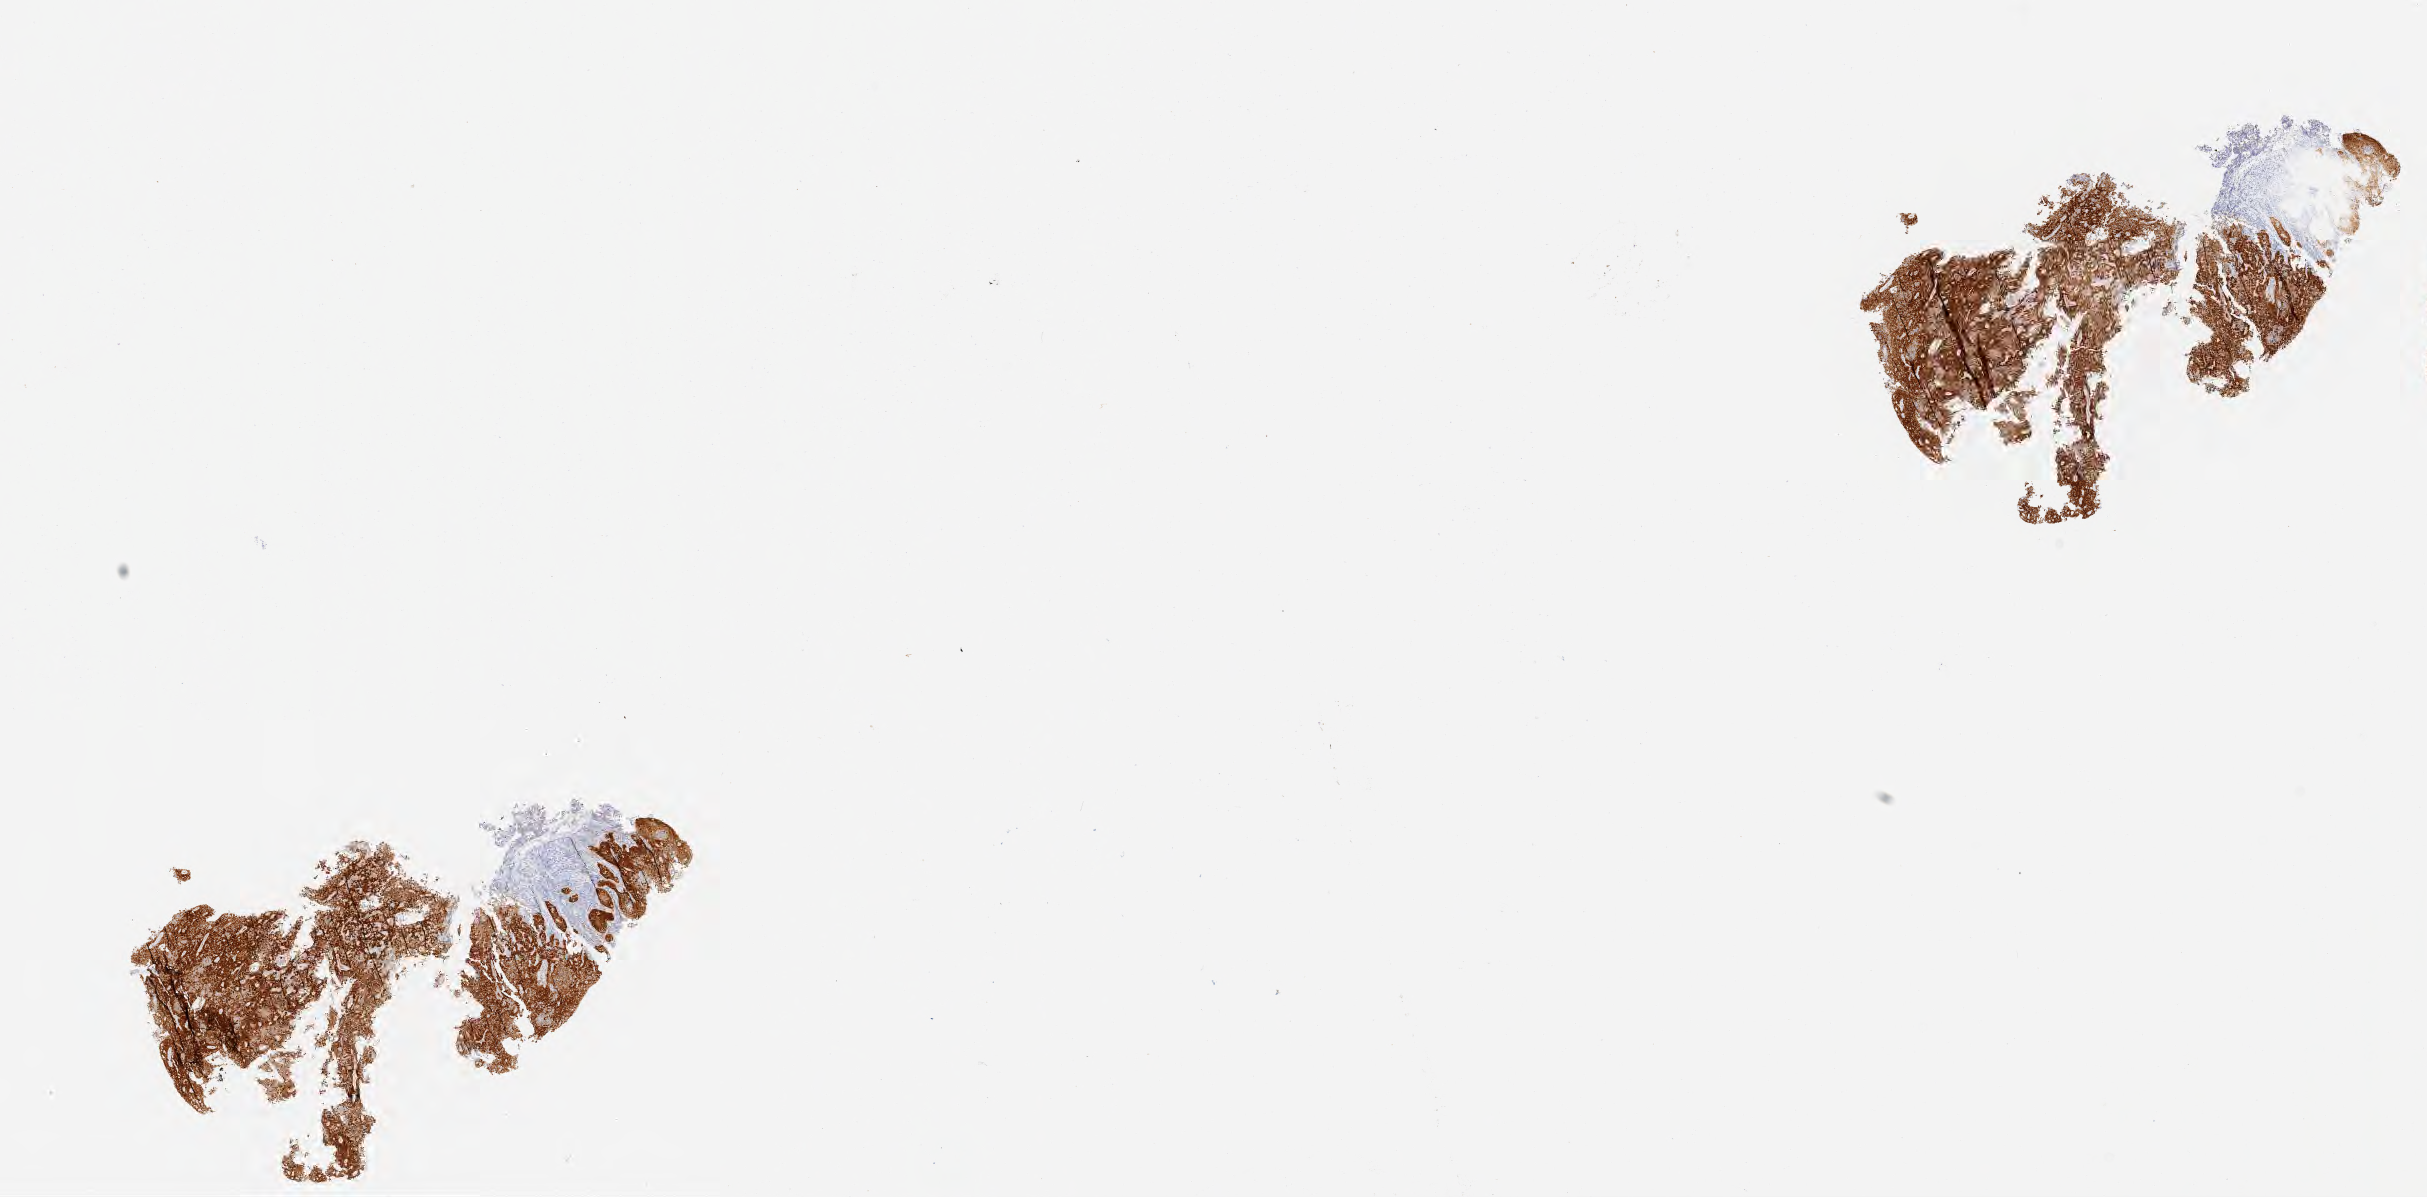
Whole-slide image, immunohistochemical stain for p16 (p16INK4a) — shown as a low-resolution overview of the whole scanned area (about 19.6 x 9.7 mm), specimen: tumor tissue, anatomic site: cervix. Patient female; aged 39.
Histologic diagnosis: Squamous cell carcinoma, large cell, nonkeratinizing, NOS.